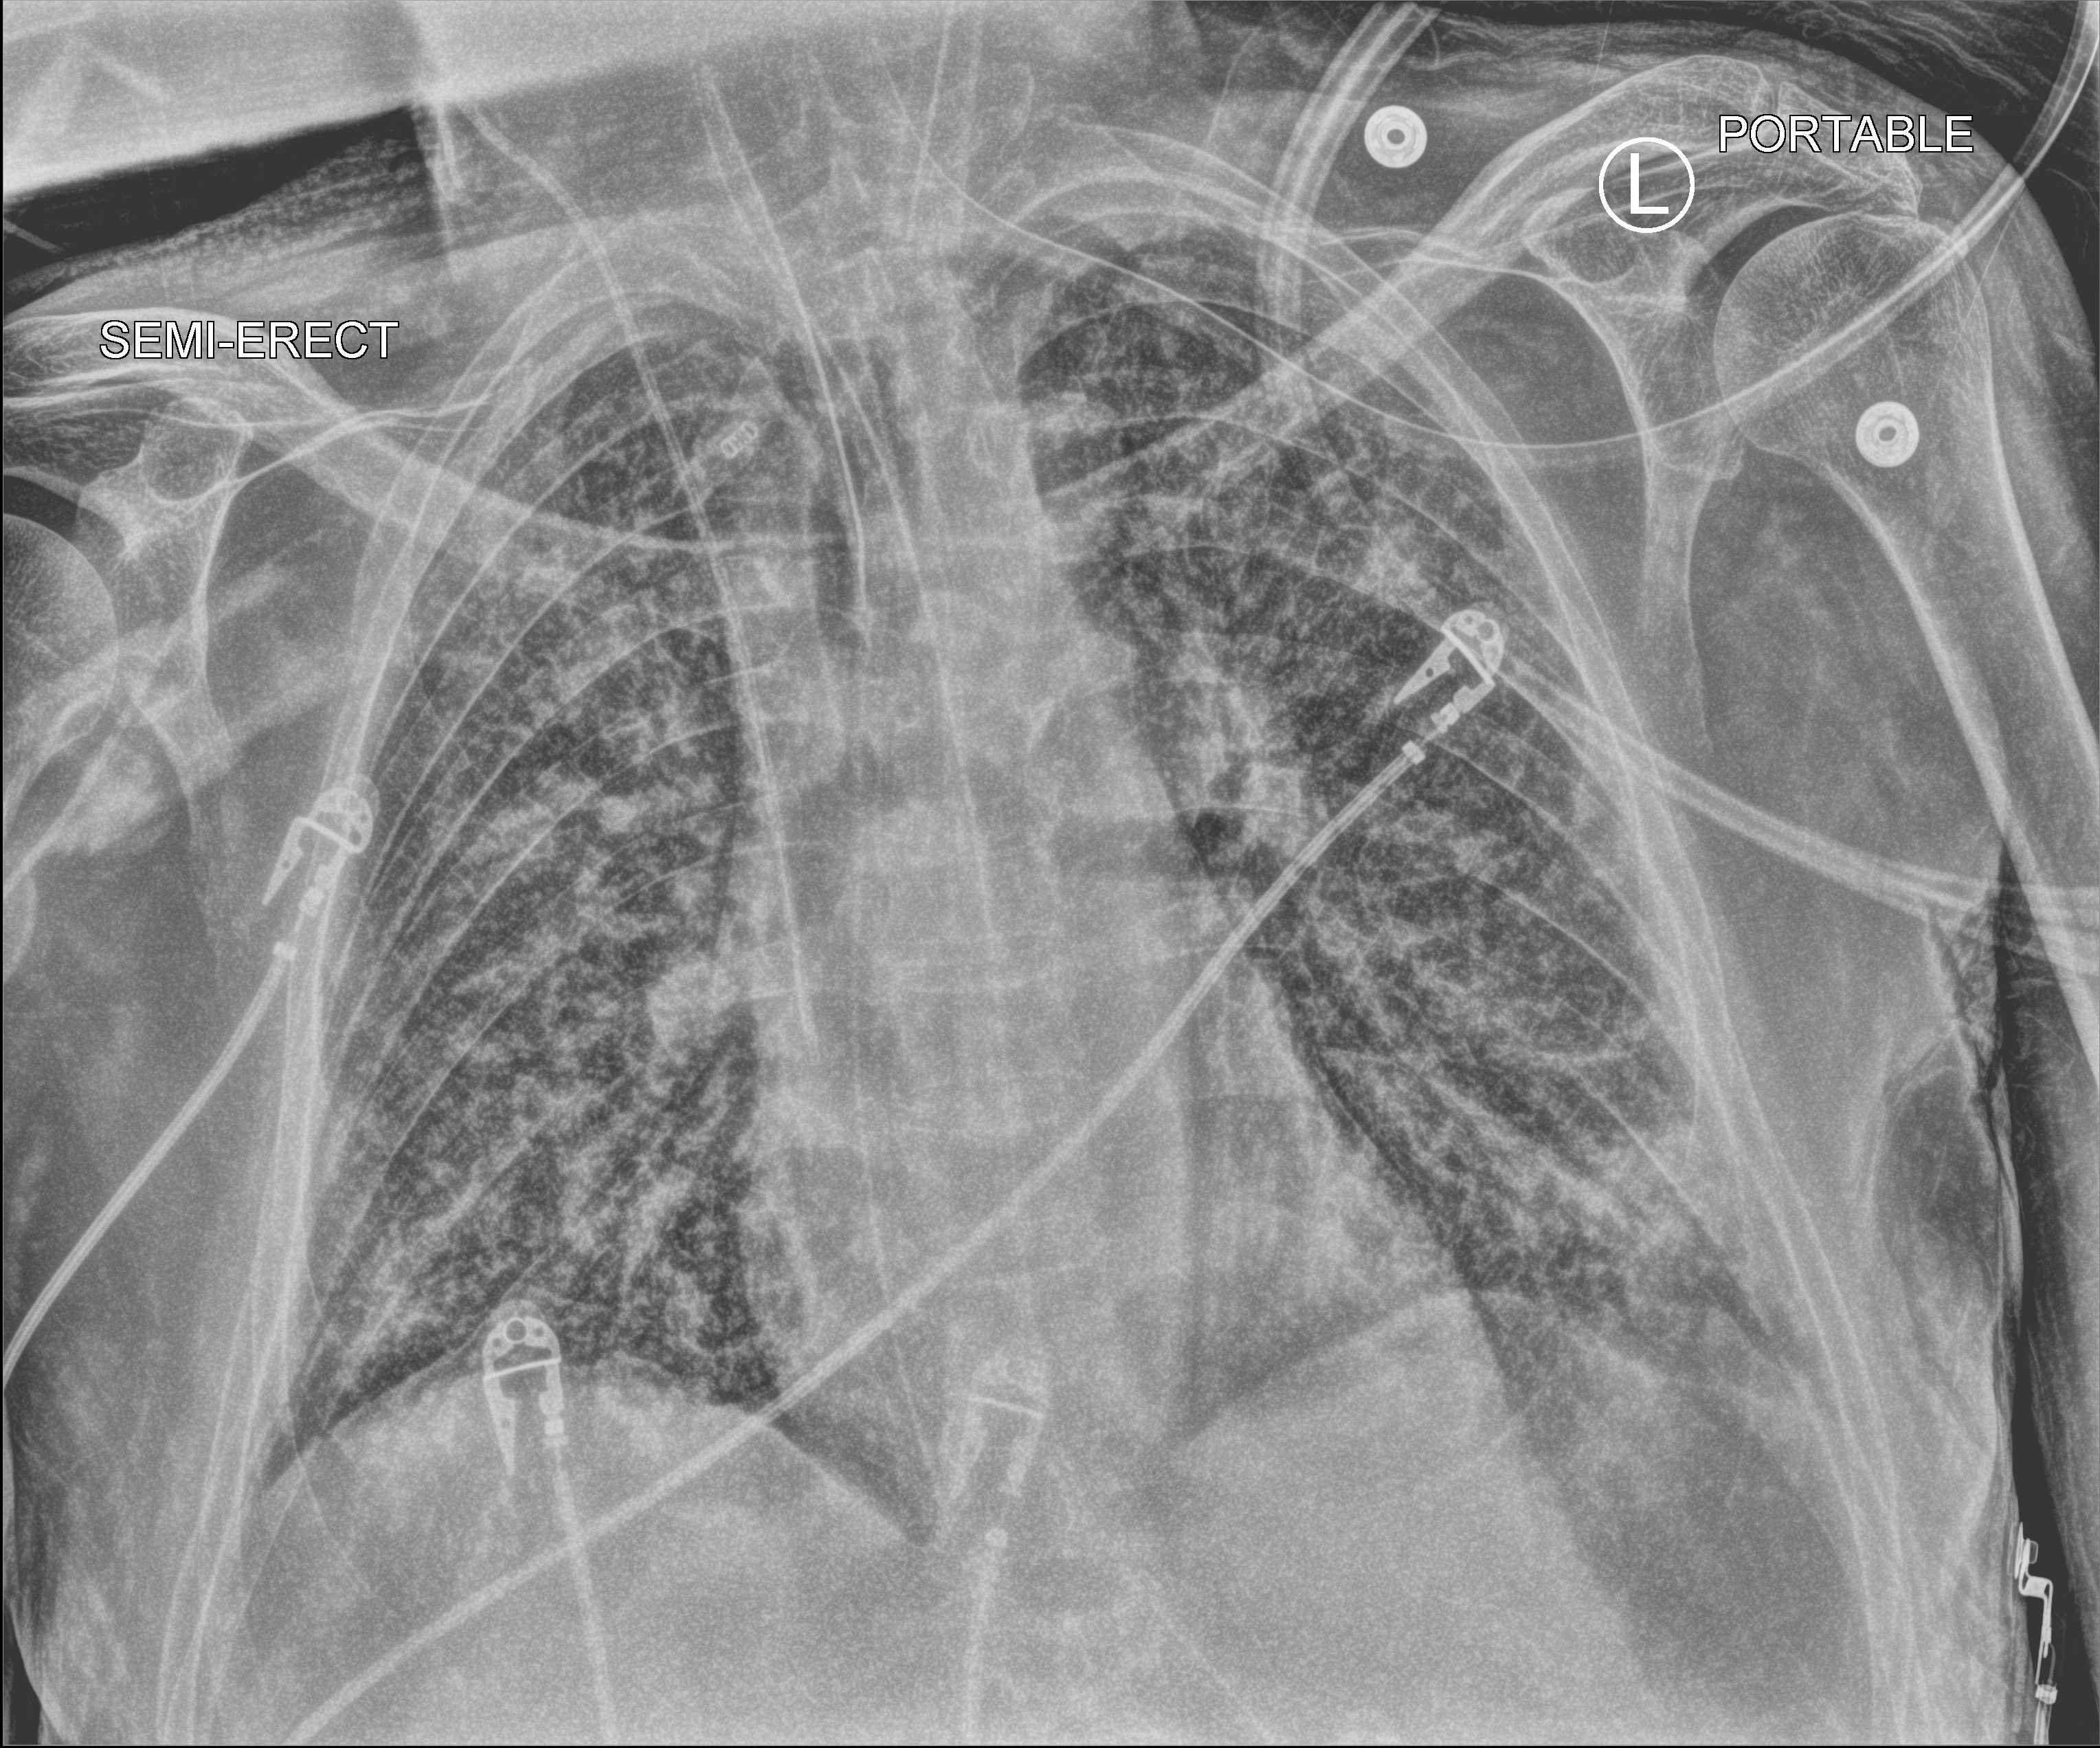
Chest X-ray (portable), anteroposterior (AP) projection. Patient hospitalised with COVID-19; male, aged 60–74 years.
Admission-level facts for this patient (not findings on this image; timing relative to this image not recorded):
- COPD (admission record): no